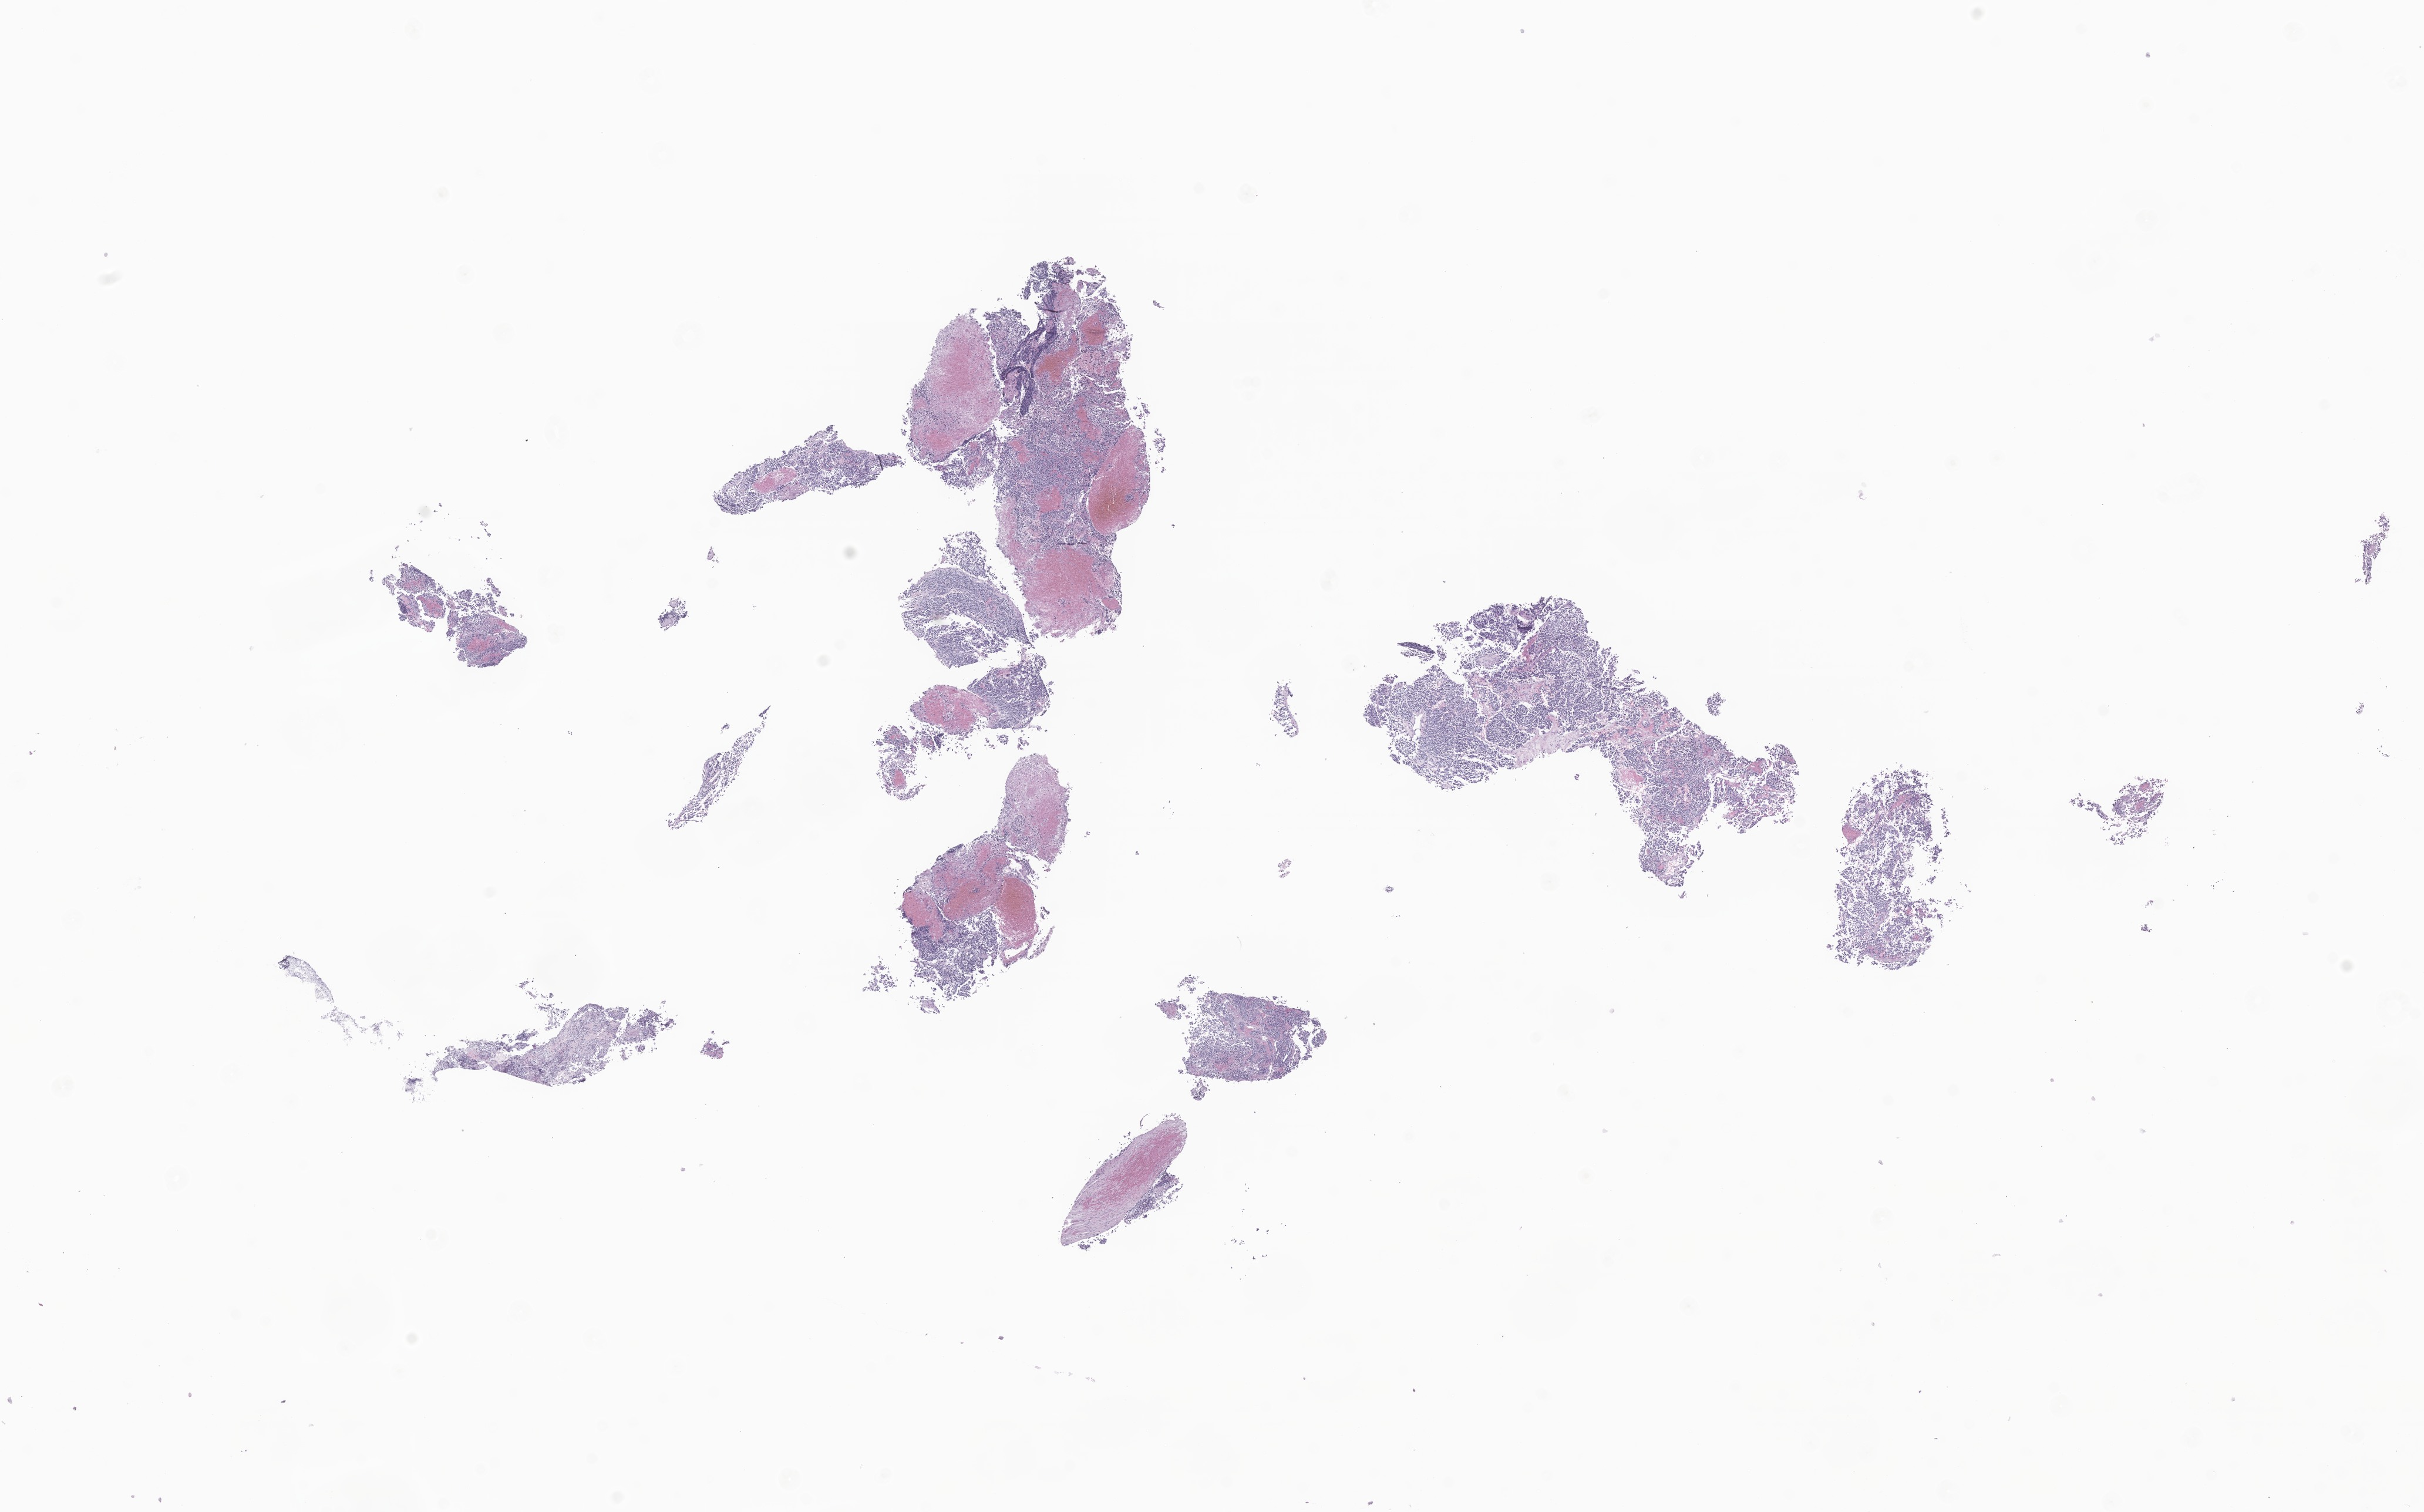
Digitized hematoxylin and eosin (H&E)-stained section of tumor tissue from the abdomen, whole scanned area (about 17.4 x 10.9 mm) shown as a low-resolution overview. Formalin-fixed paraffin-embedded section. Male patient, age 906 days (about 2.5 years).
• diagnosis: Neuroblastoma, NOS